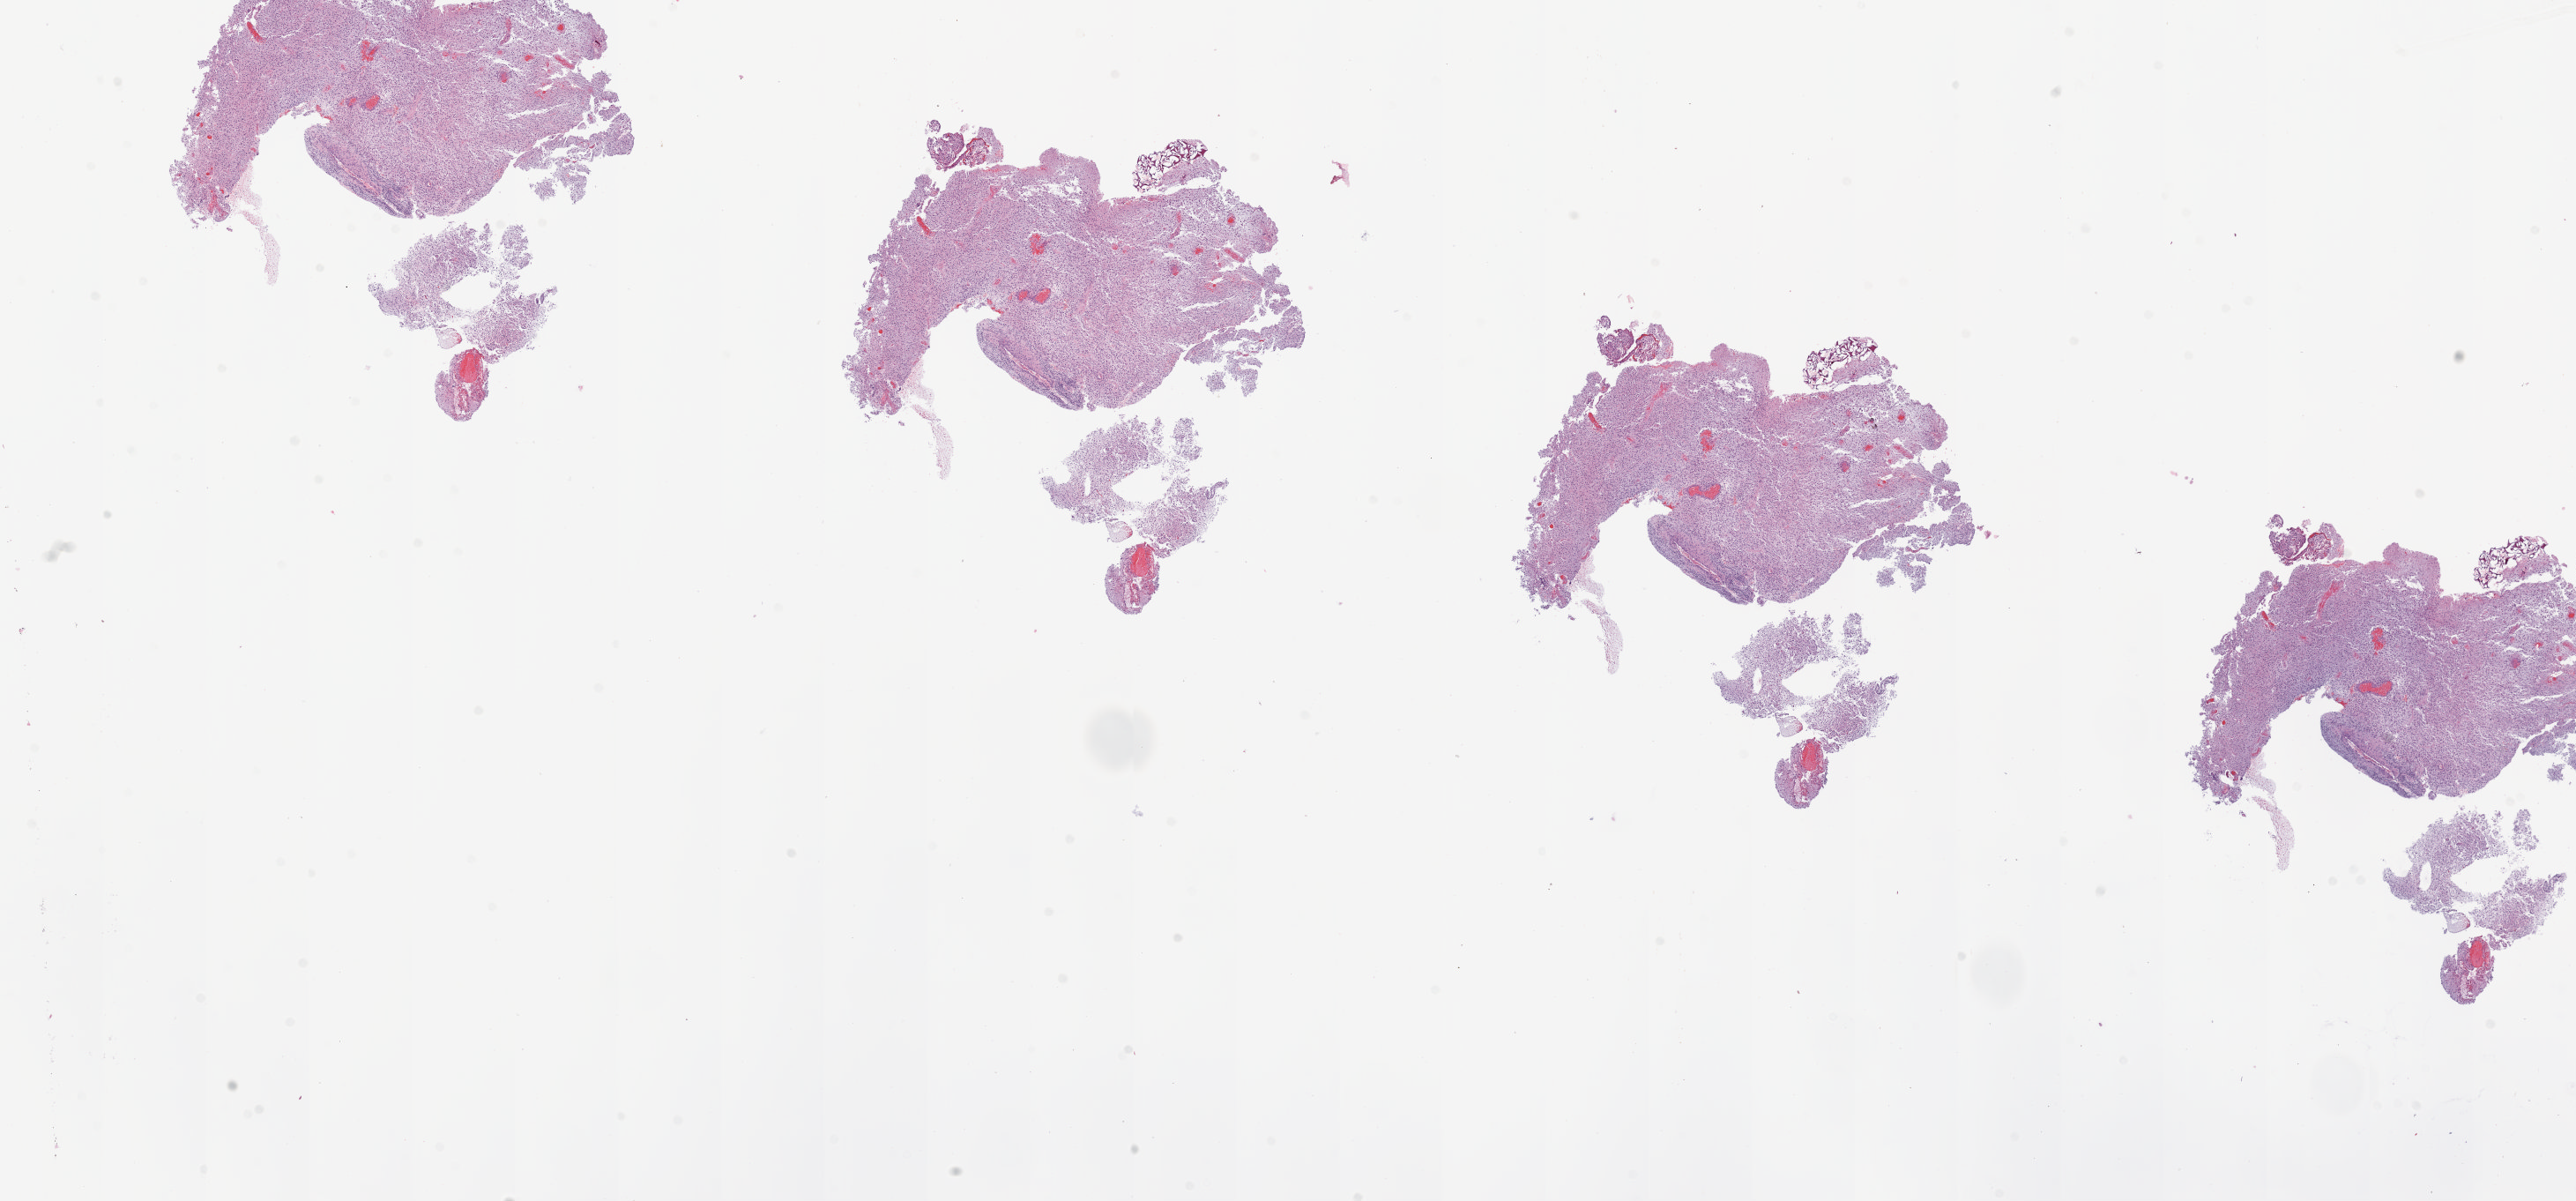
Whole-slide histology image, Hematoxylin and eosin (H&E) stained — low-resolution overview of the scanned area, about 23.4 x 10.9 mm; frozen section from the top of the tissue portion; sample: primary tumour, brain. Male, age 61 years at initial diagnosis. Pathologist review of this section (percent, as recorded): tumour cells 100%, tumour nuclei 85%, normal cells 0%, stromal cells 0%, necrosis 0%.
Pathologic diagnosis: Glioblastoma.